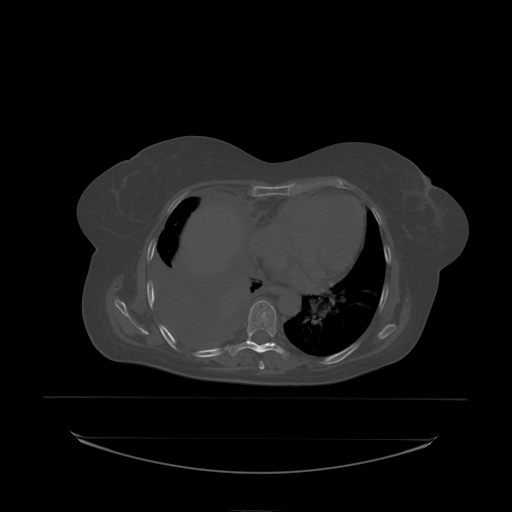
CT including the spine, one axial slice; position 133 of 242 along the scan axis; bone window (W 1800 / L 400 HU); 2.5 mm slice thickness; 512 × 512 image matrix, field of view 500 × 500 mm. Patient: female, 53 years. Case-level facts recorded for this patient, not image findings: primary cancer: lung; vertebrae with lytic lesions (as recorded): T7, L1.
Outlined on this slice (semi-automatically segmented with operator editing):
- T8 vertebra: bounding box (x1, y1, x2, y2) in pixels: (247, 300, 277, 338)